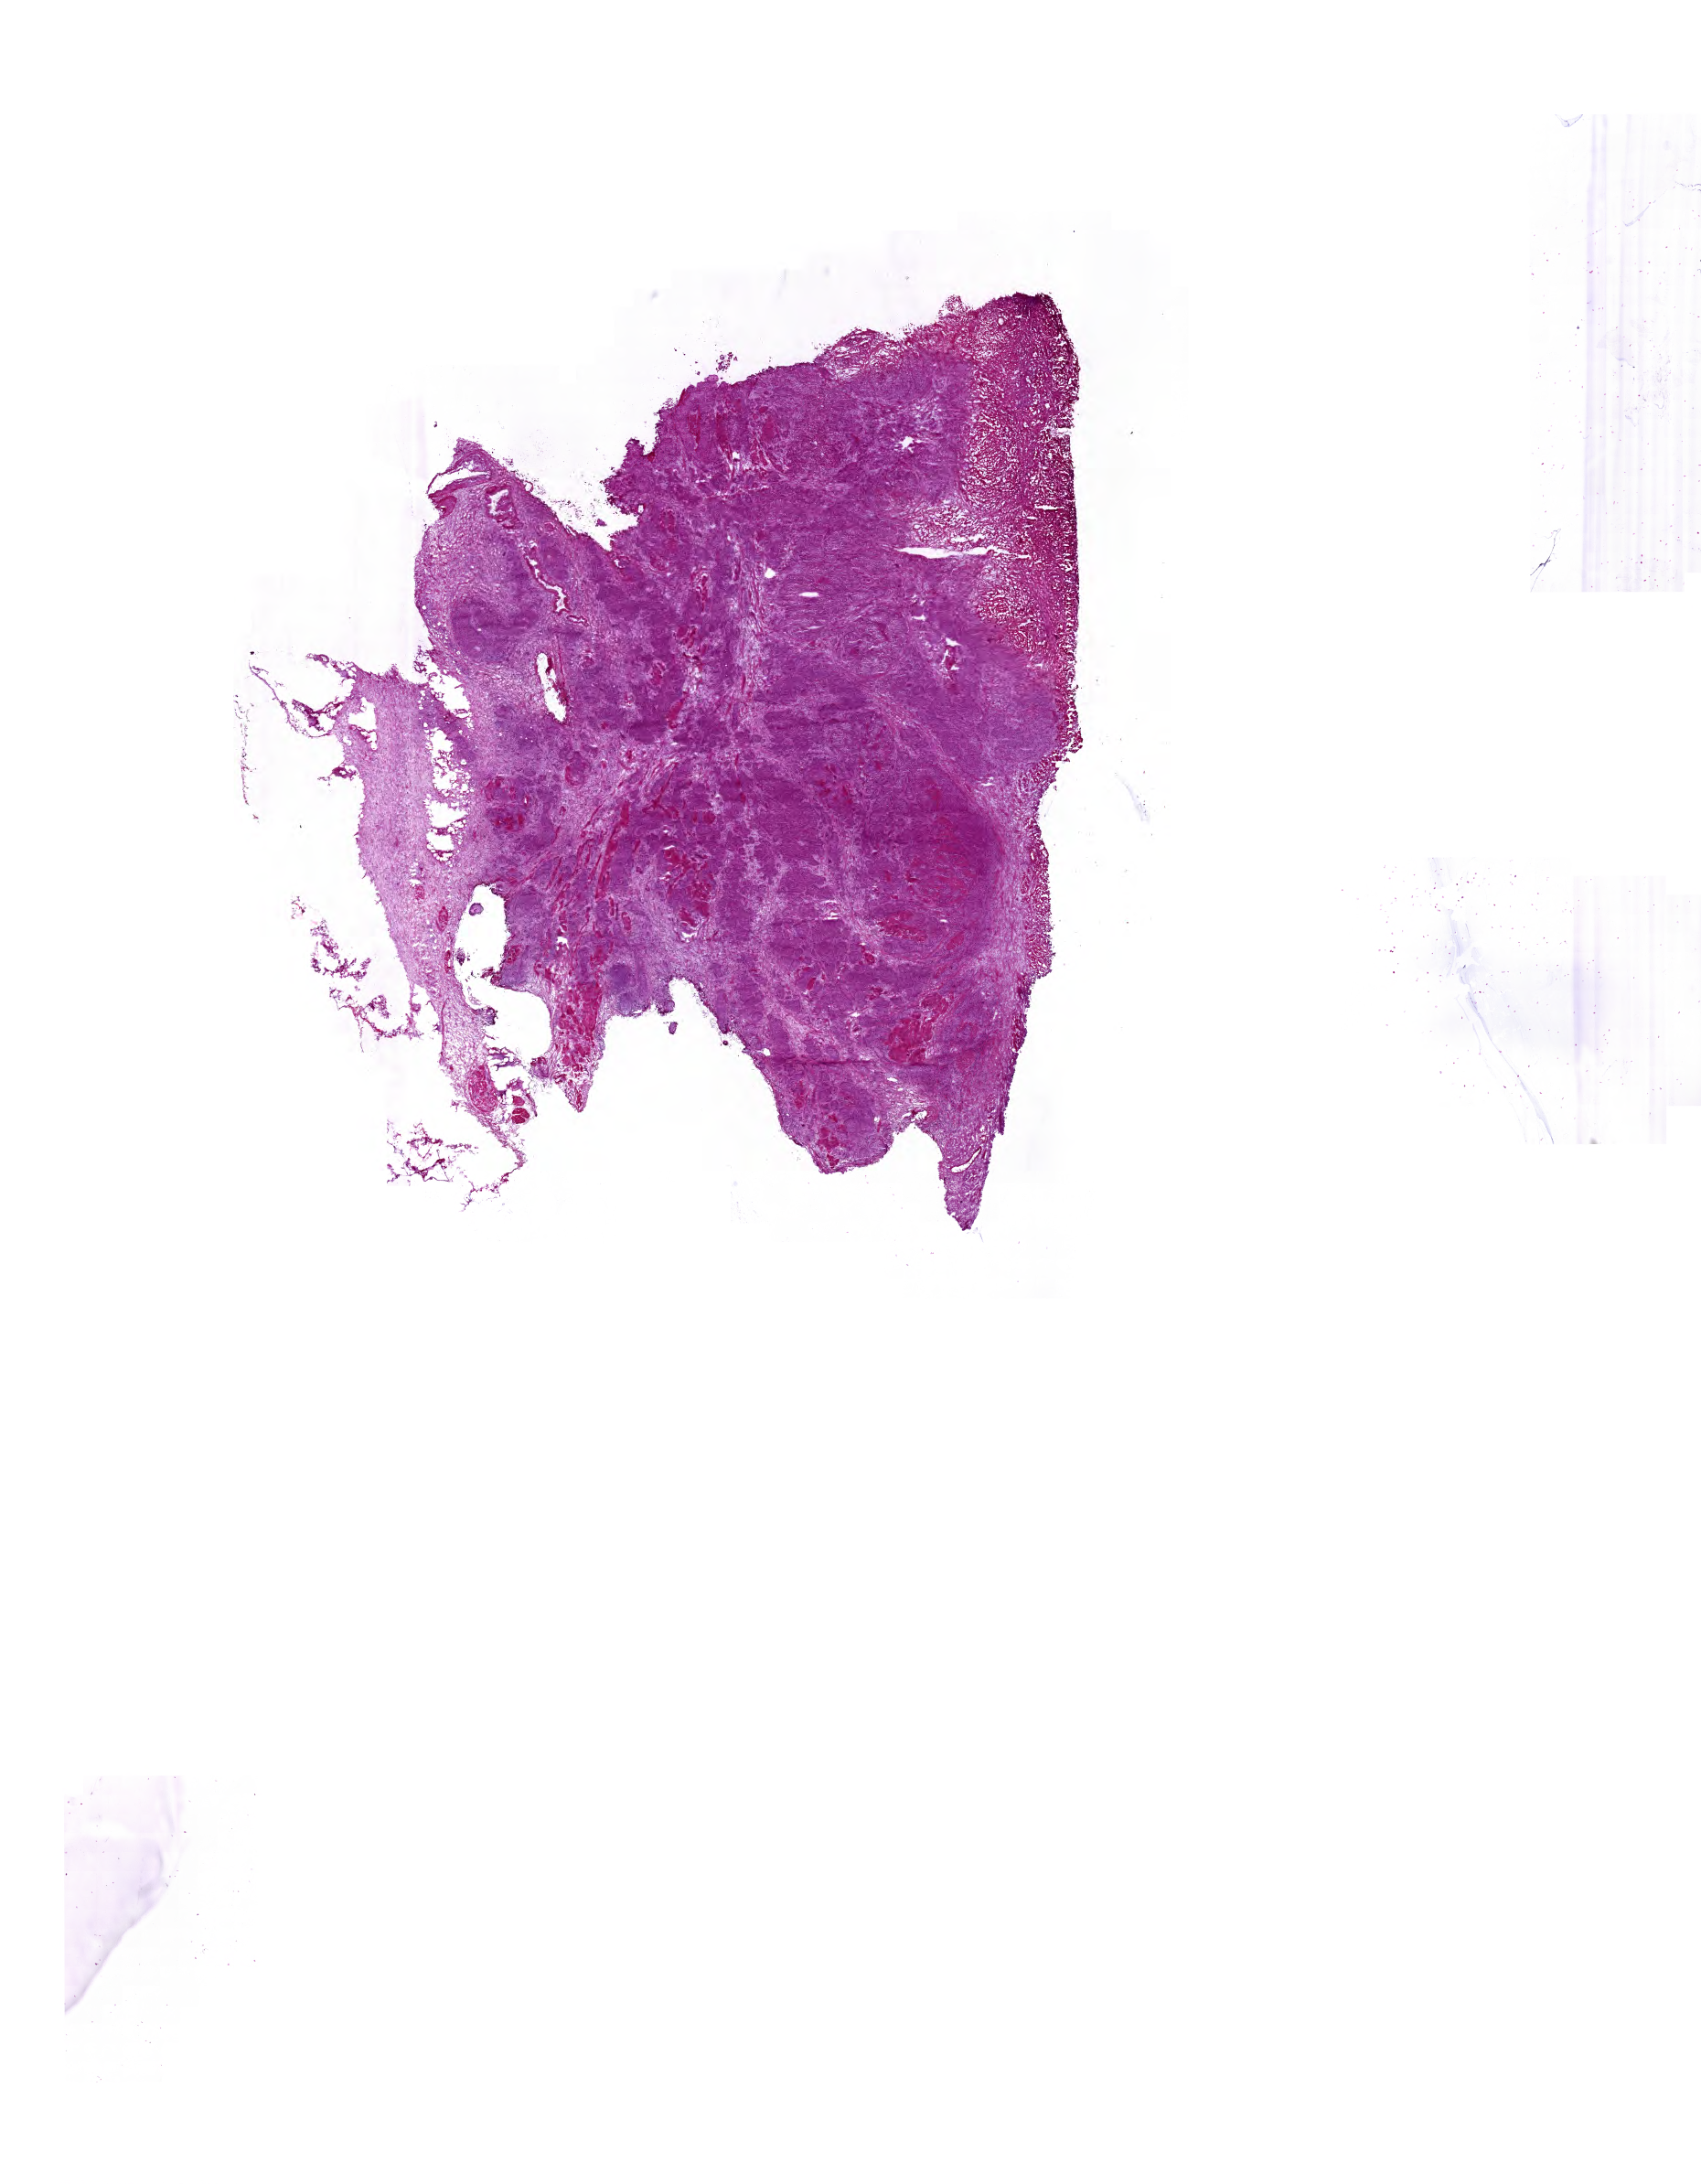
Digitized H&E tissue section (whole slide) — low-resolution overview of the scanned area, about 23.2 x 29.7 mm (slide scanned at 40x); formalin-fixed paraffin-embedded (FFPE) diagnostic section; primary tumour sample from the bladder. Female, age 73 years at initial diagnosis.
Diagnosis: Transitional cell carcinoma.